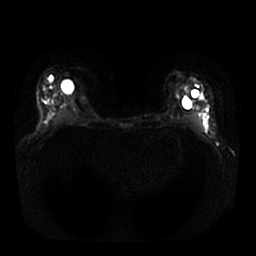
Breast MRI, one axial slice. Position 18 of 25 along the scan axis. Diffusion-weighted series; image 2 of 4 stored at this slice position (different b-values; order by instance number). 1.5 T. 4 mm slice thickness. 256 × 256 image matrix, field of view 340 × 340 mm. Female patient.
Annotated regions visible in this slice (manually delineated by an expert):
- tumour on diffusion-weighted imaging: bounding box (x1, y1, x2, y2) in pixels: (193, 88, 208, 123)